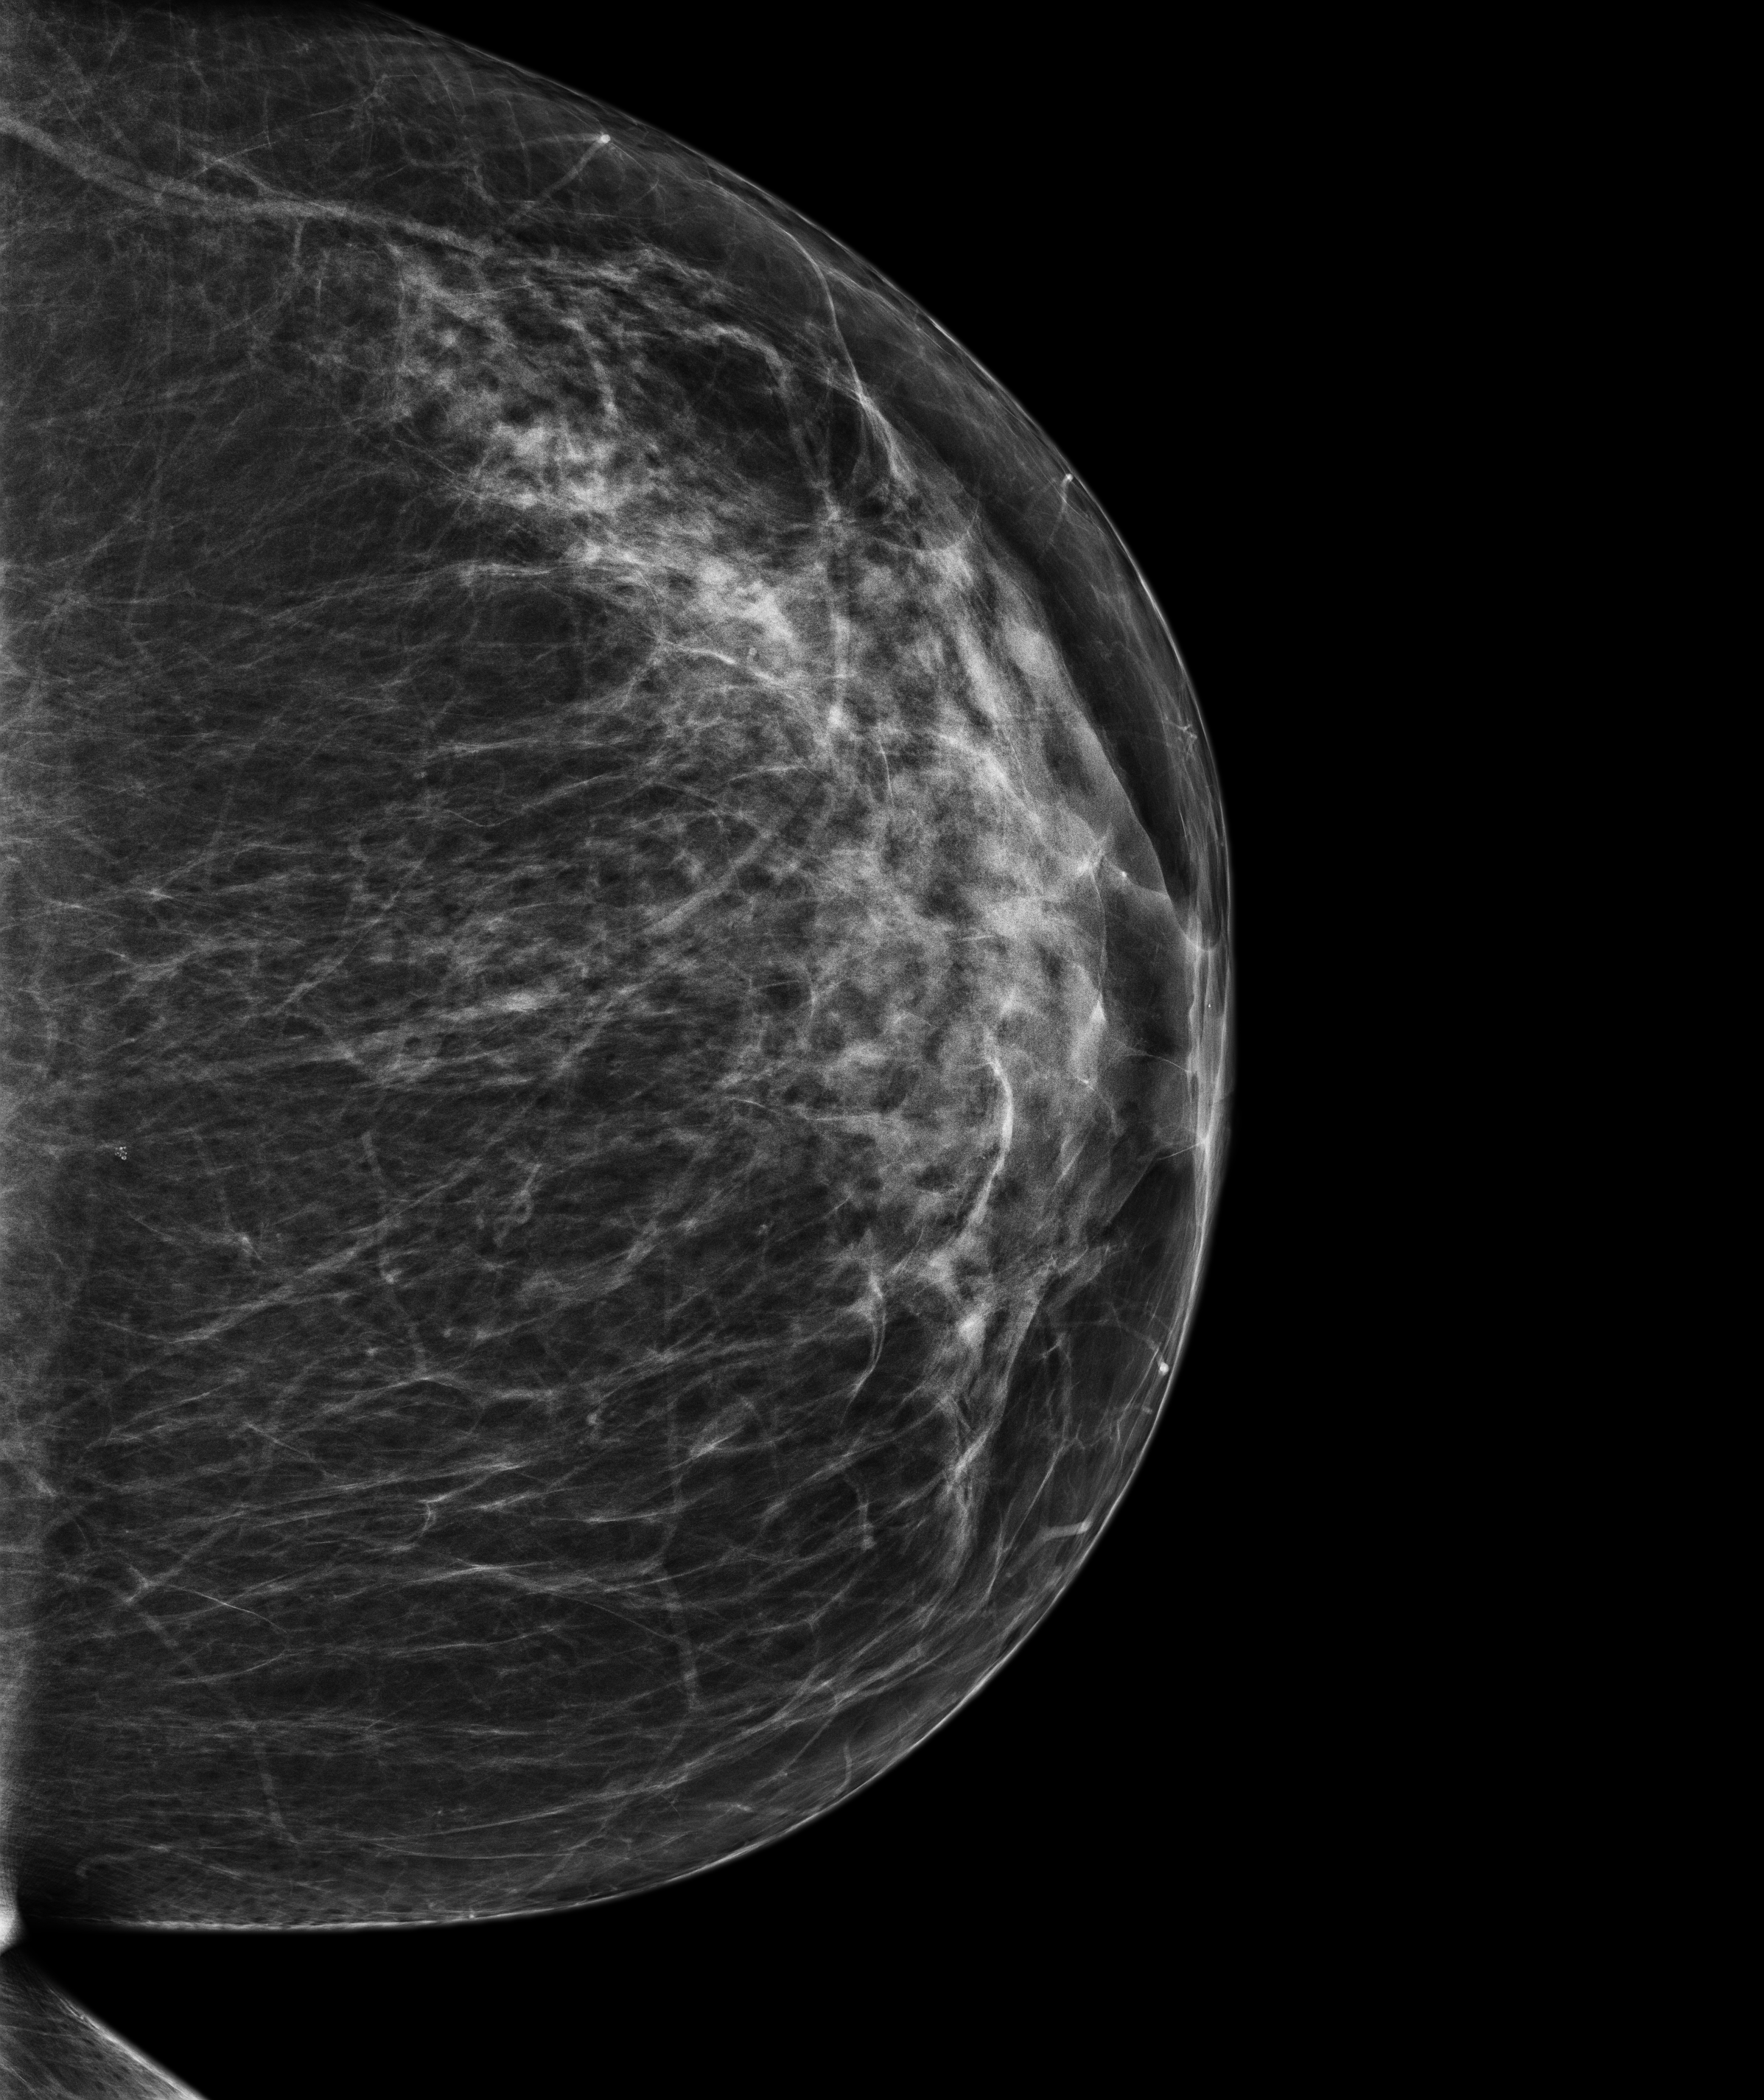
Screening examination, compressed breast thickness 66 mm. Patient: female, 57 years.
Image type: full-field digital mammogram. Breast: left. Projection: cranio-caudal projection.